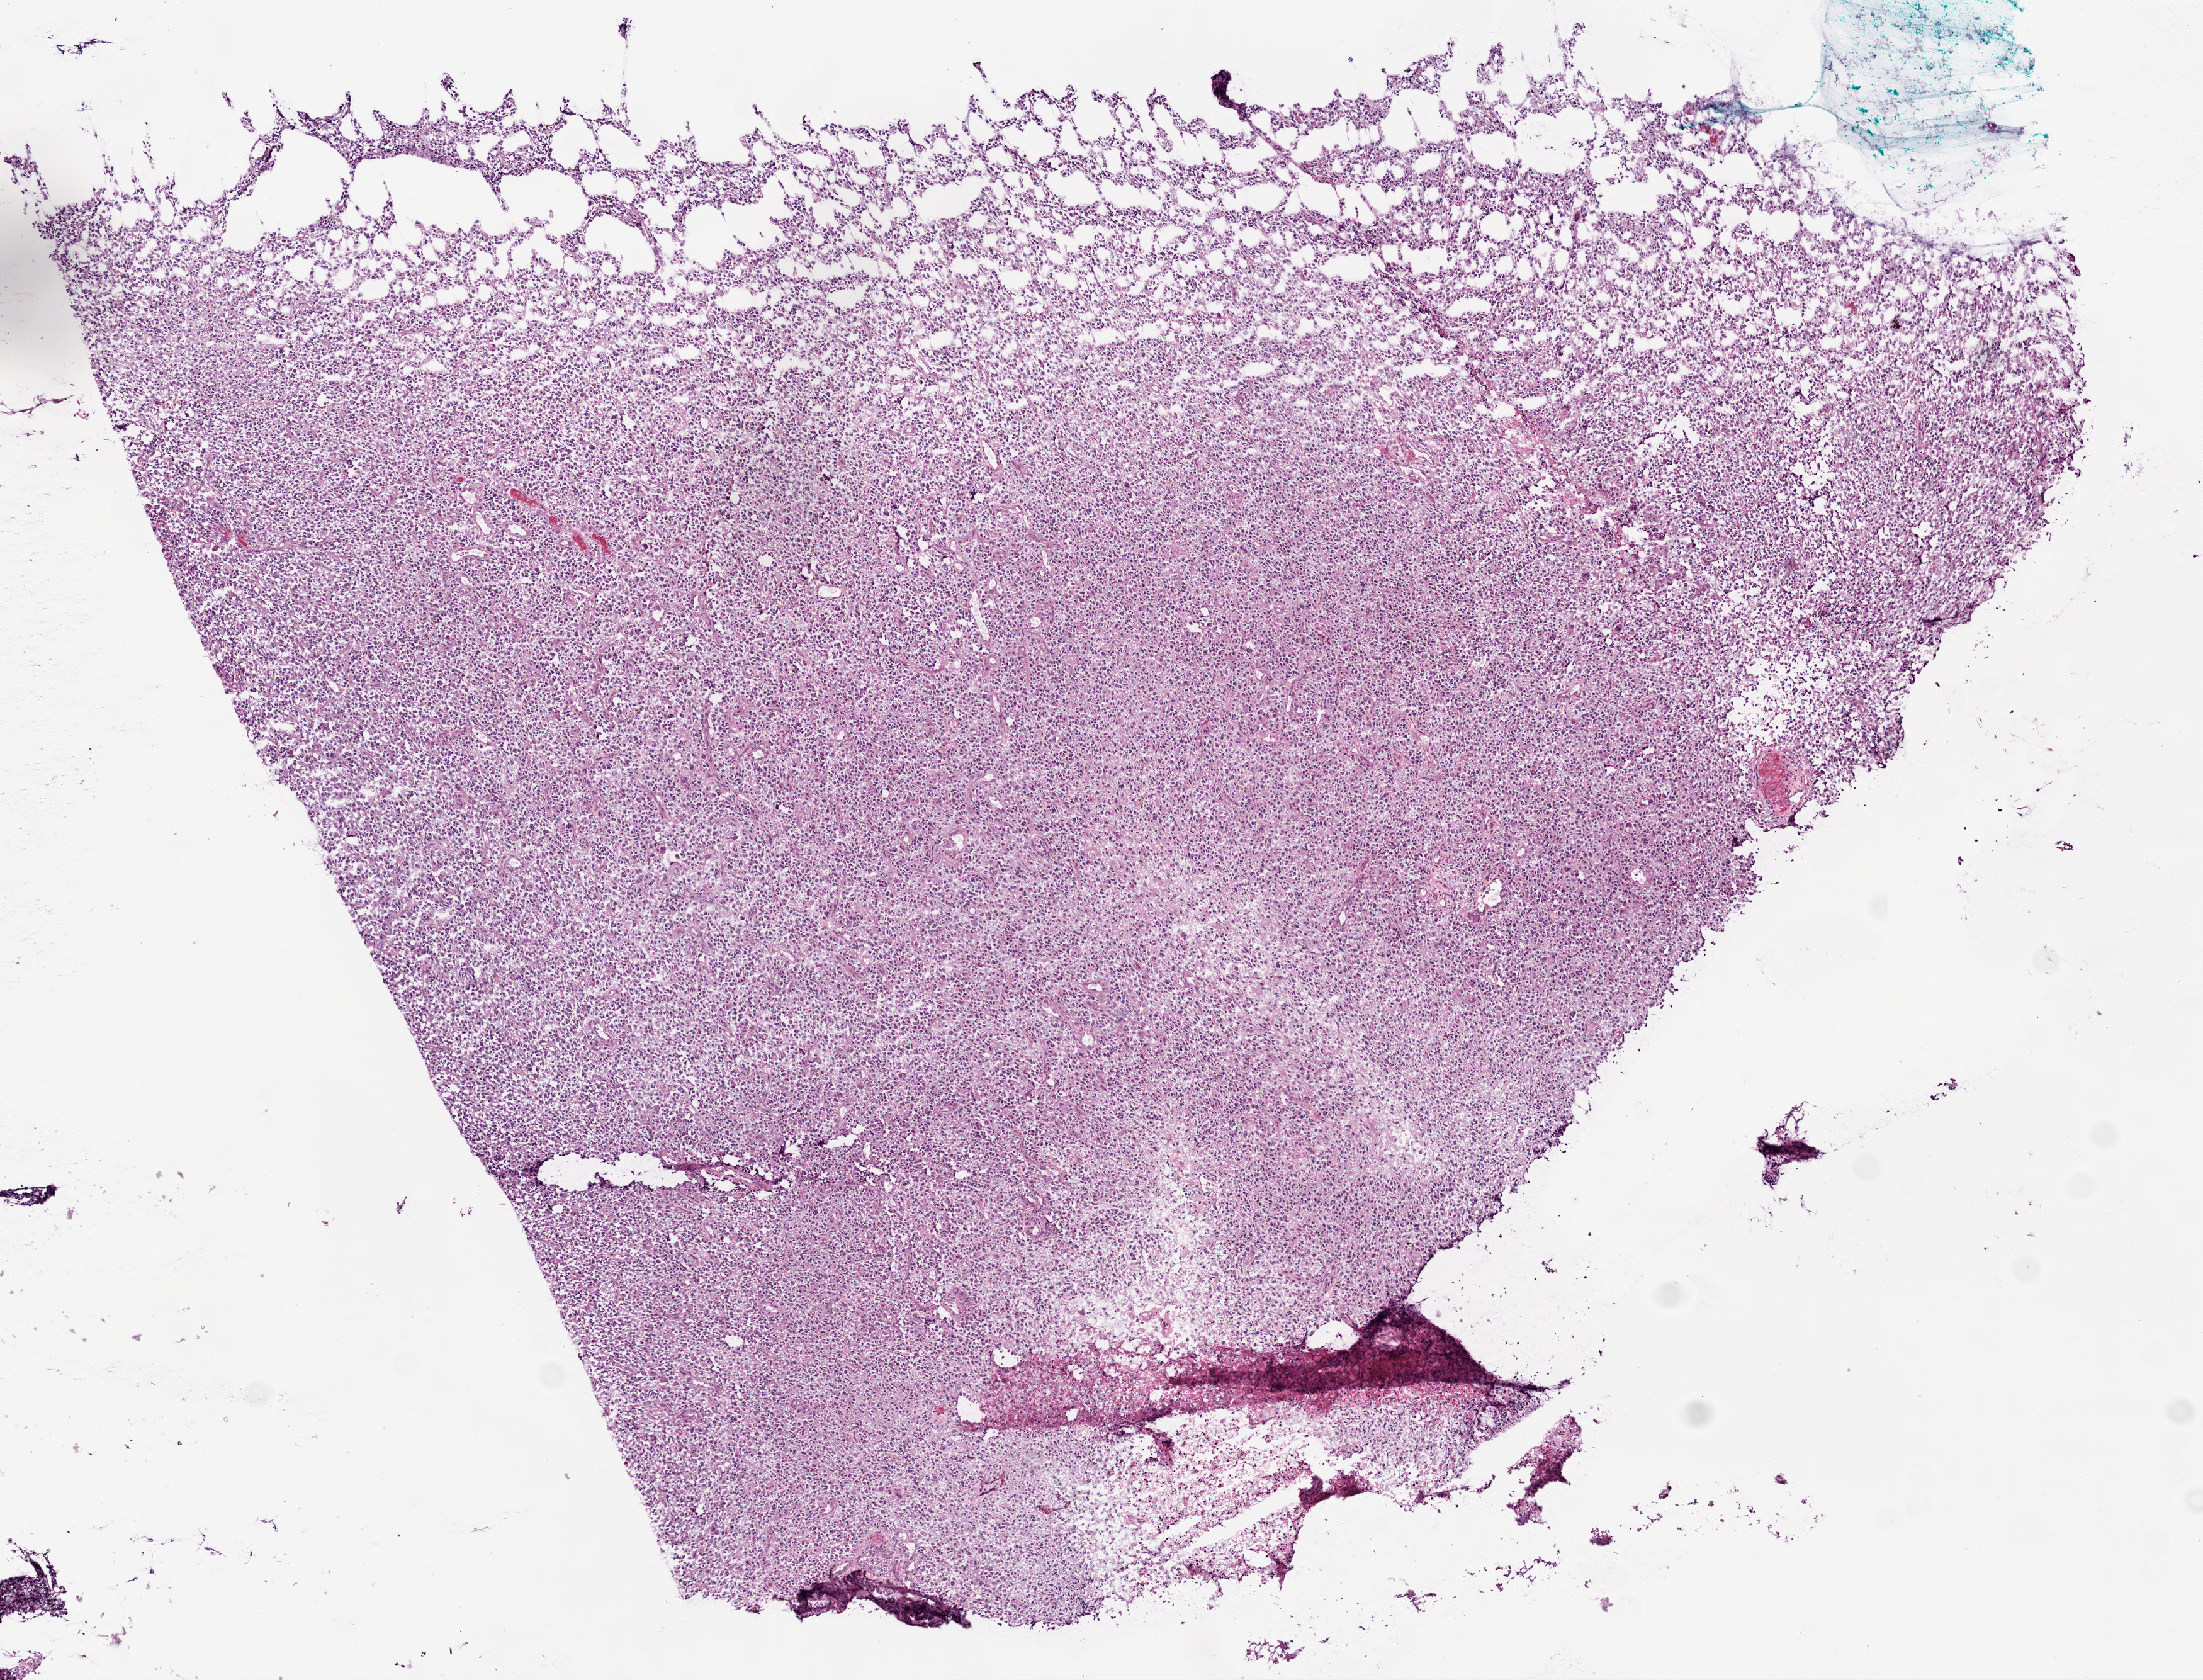
H&E-stained whole-slide image, shown as a low-resolution overview of the whole scanned area (about 7.0 x 5.4 mm). Frozen section from the bottom of the tissue portion. Primary tumour sample from the brain. Patient: male, age at initial diagnosis 72 years. Composition of this section per pathologist review: tumour cells 95%, tumour nuclei 95%, normal cells 0%, stromal cells 0%, necrosis 5%.
Pathologic diagnosis: Glioblastoma.